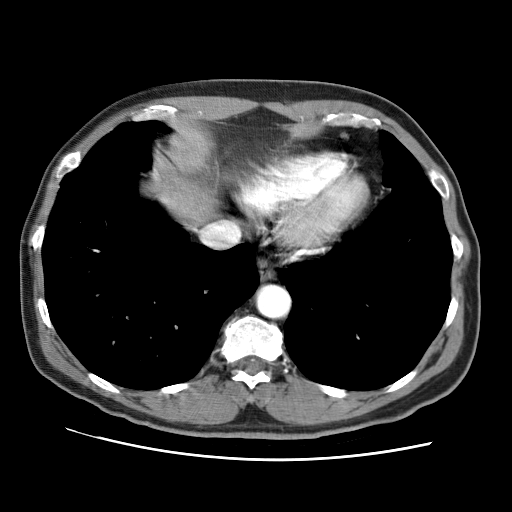
Contrast-enhanced abdominal CT (liver protocol), one axial slice. Reconstruction kernel STANDARD. Soft-tissue window (W 400 / L 40 HU). 2.5 mm slice thickness. 512 × 512 image matrix. From the clinical record (not read from this slice): diagnosis: hepatocellular carcinoma (patient treated with transarterial chemoembolisation; whether this scan precedes or follows treatment is not stated here); TNM stage (as recorded): Stage-II.
Outlined on this slice (semi-automatic segmentation, software-assisted and operator-edited):
- liver parenchyma outside the tumour (the mass and vessels are separate outlines, so this box may not span the whole liver): box from (x=150, y=128) to (x=212, y=222) px